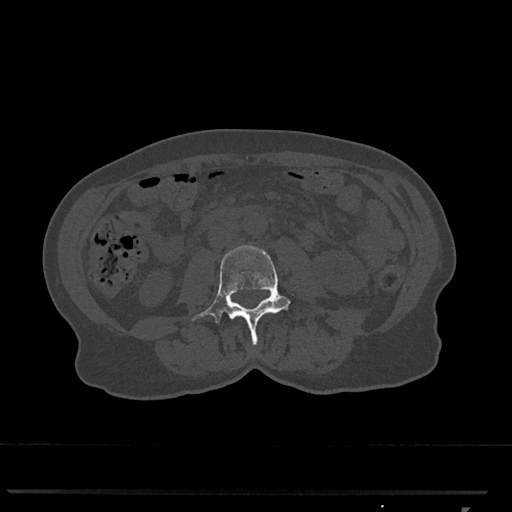
CT including the spine, one axial slice; slice 273 of 793 in the series (ordered by position); reconstruction kernel Br40s/3; bone window (W 1800 / L 400 HU); 0.5 mm slice thickness; 512 × 512 image matrix, field of view 380 × 380 mm. Female patient, age 62 years. From the clinical record (not read from this slice): primary cancer: renal.
Outlined on this slice (semi-automatically segmented with operator editing):
- L3 vertebra: box from (x=192, y=245) to (x=291, y=345) px